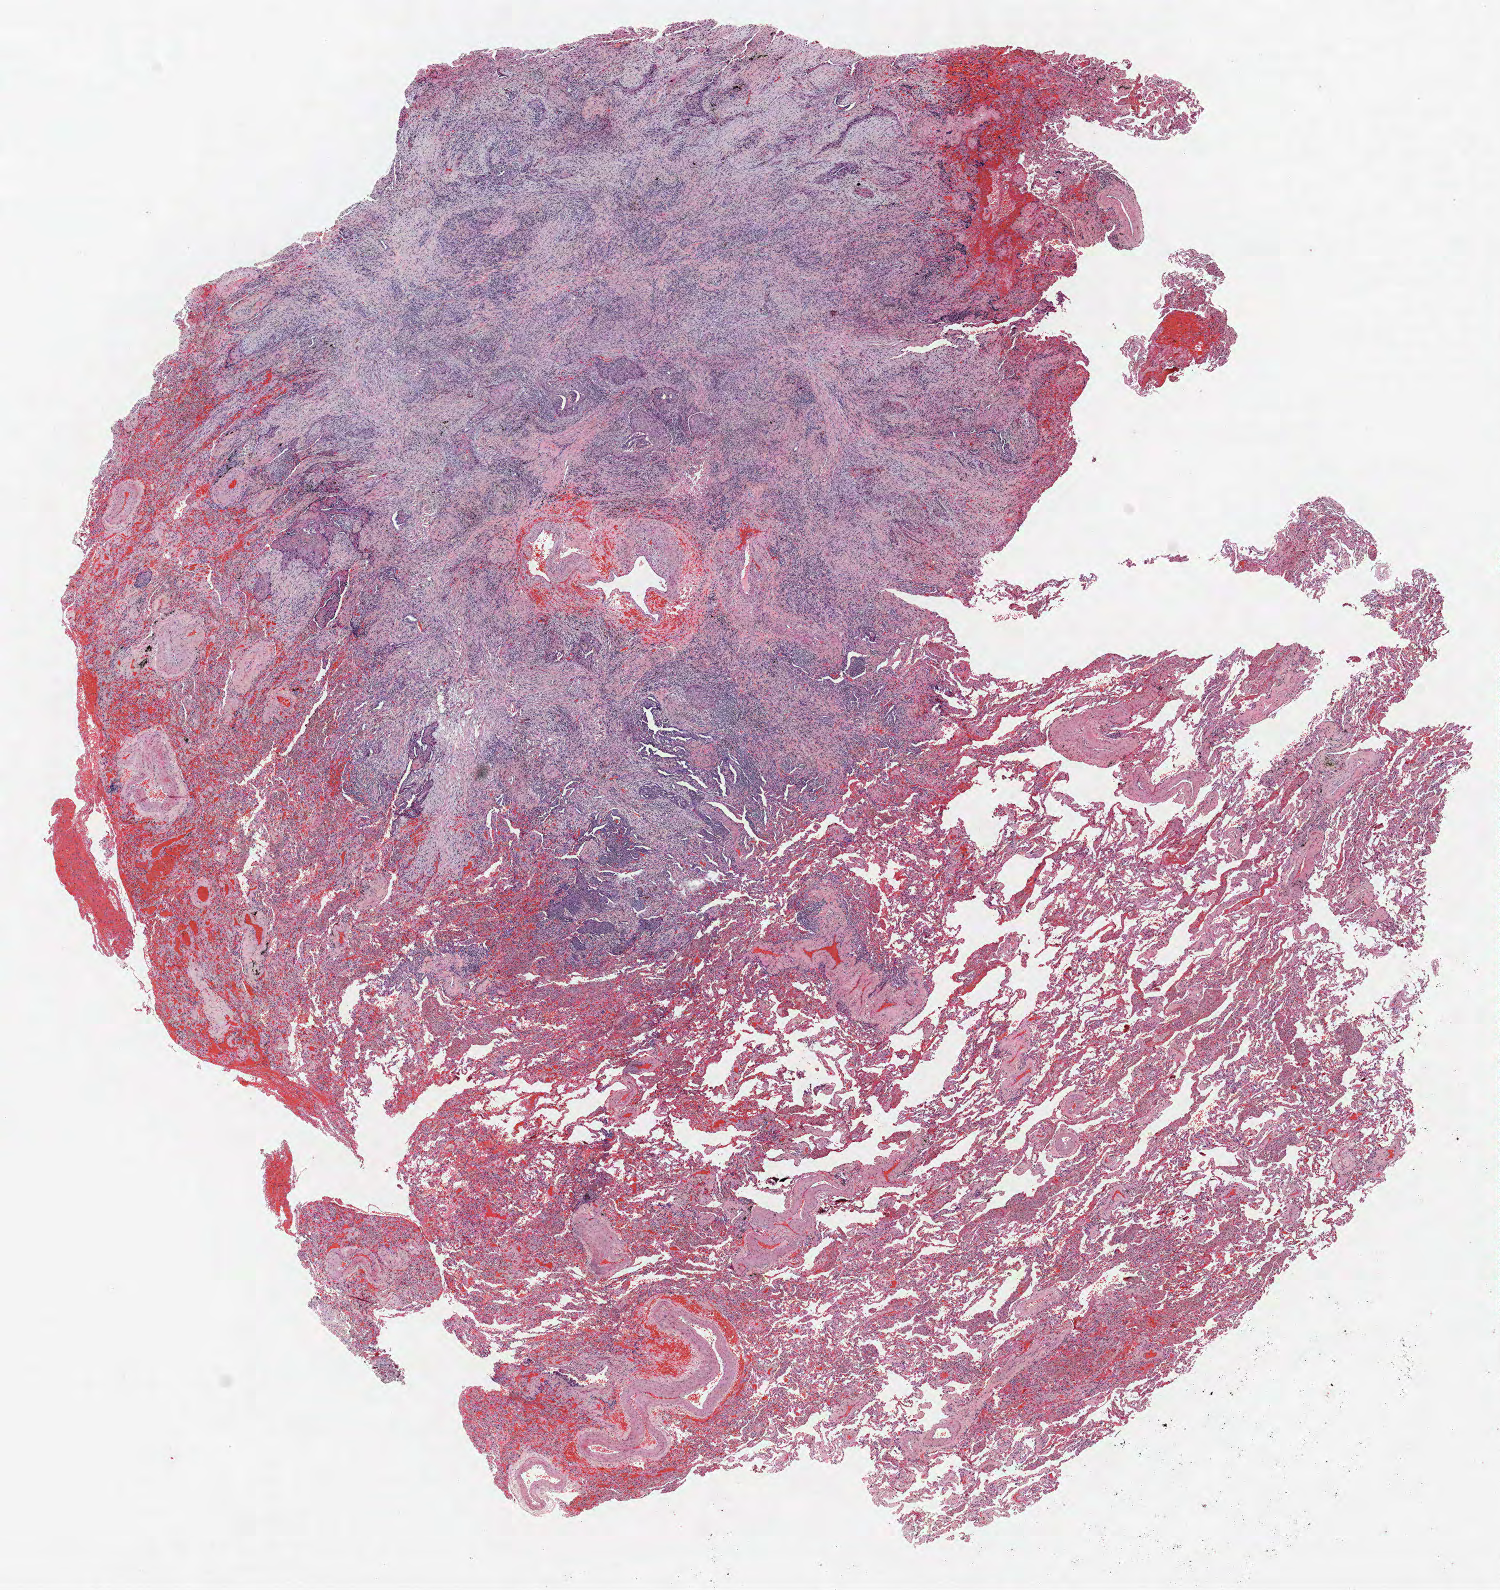
Whole-slide histology image, Hematoxylin and eosin (H&E) stained, shown as a low-resolution overview of the whole scanned area (about 12.0 x 12.7 mm, slide scanned at 40x); formalin-fixed paraffin-embedded (FFPE) section; lung tissue. Male, age 64 at enrolment. Current smoker at enrolment. Grade: moderately differentiated (G2).
• tumour size (pathology): 10 mm
• primary tumour location (clinical record): left upper lobe
• participant's lung-cancer diagnosis: Squamous cell carcinoma, NOS
• stage (AJCC 6th edition): IA